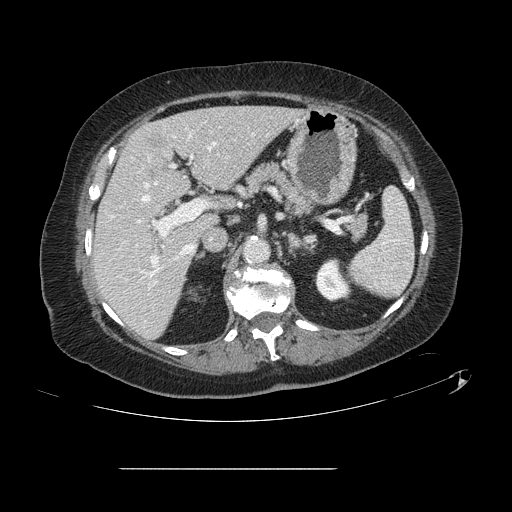
Contrast-enhanced abdominal CT, one axial slice. Slice 74 of 148 in the series (ordered by position). 120 kVp. Intravenous contrast given. Soft-tissue window (W 400 / L 40 HU). 2.5 mm slice thickness. 512 × 512 image matrix, field of view 439 × 439 mm. Female patient, age 75 years. From the clinical record (not read from this slice): diagnosis: colorectal cancer liver metastases, imaged before liver resection; multiple liver metastases: no; largest metastasis: 2.4 cm; chemotherapy before resection: no.
Annotated regions visible in this slice (manually delineated by an expert):
- hepatic veins: bounding box (x1, y1, x2, y2) in pixels: (143, 143, 215, 253)
- liver: (93, 107, 297, 338)
- planned liver remnant (the part of the liver to remain after resection): (93, 107, 296, 338)
- portal vein (with intrahepatic branches): (136, 157, 204, 276)
- liver metastasis: (150, 138, 160, 148)